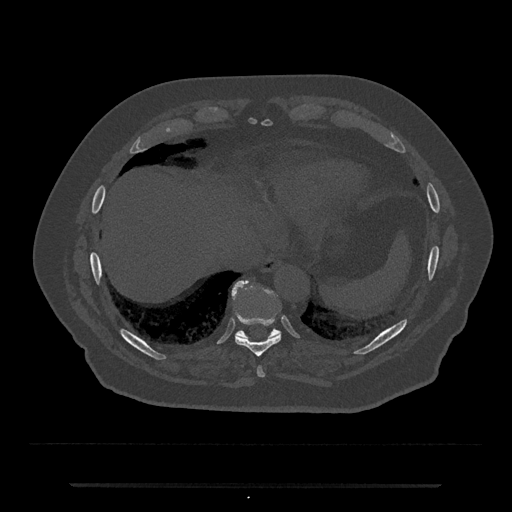
CT including the spine, one axial slice. 120 kVp. Bone window (W 1800 / L 400 HU). 0.5 mm slice thickness. 512 × 512 image matrix. Patient: male, 80 years. Case-level facts recorded for this patient, not image findings: primary cancer: prostate.
Structures marked on this image (semi-automatic segmentation, software-assisted and operator-edited):
- T10 vertebra: box from (x=232, y=281) to (x=281, y=339) px
- T8 vertebra: (x=257, y=367)–(x=265, y=377)
- T9 vertebra: (x=235, y=319)–(x=281, y=357)